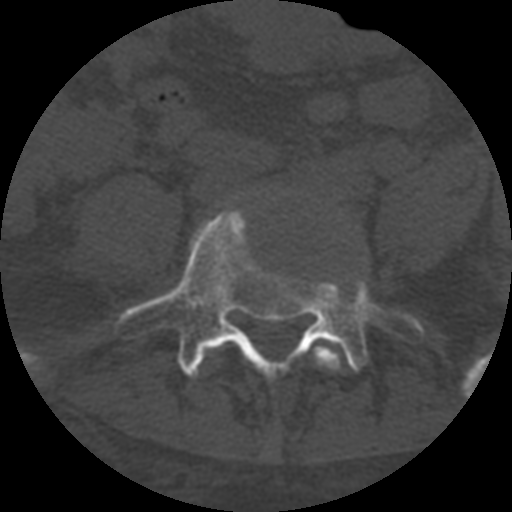
CT including the spine, one axial slice. Position 191 of 708 along the scan axis. One of 3 acquisitions stored at this slice position. Bone window (W 1800 / L 400 HU). 1.25 mm slice thickness. 512 × 512 image matrix. Patient age 55 years. Case-level facts recorded for this patient, not image findings: primary cancer: colon; vertebrae with lytic lesions (as recorded): T12, L1, L5.
Outlined on this slice (semi-automatically segmented with operator editing):
- L4 vertebra: bounding box [x1, y1, x2, y2] px = [218, 339, 346, 371]
- L5 vertebra: [114, 209, 426, 379]